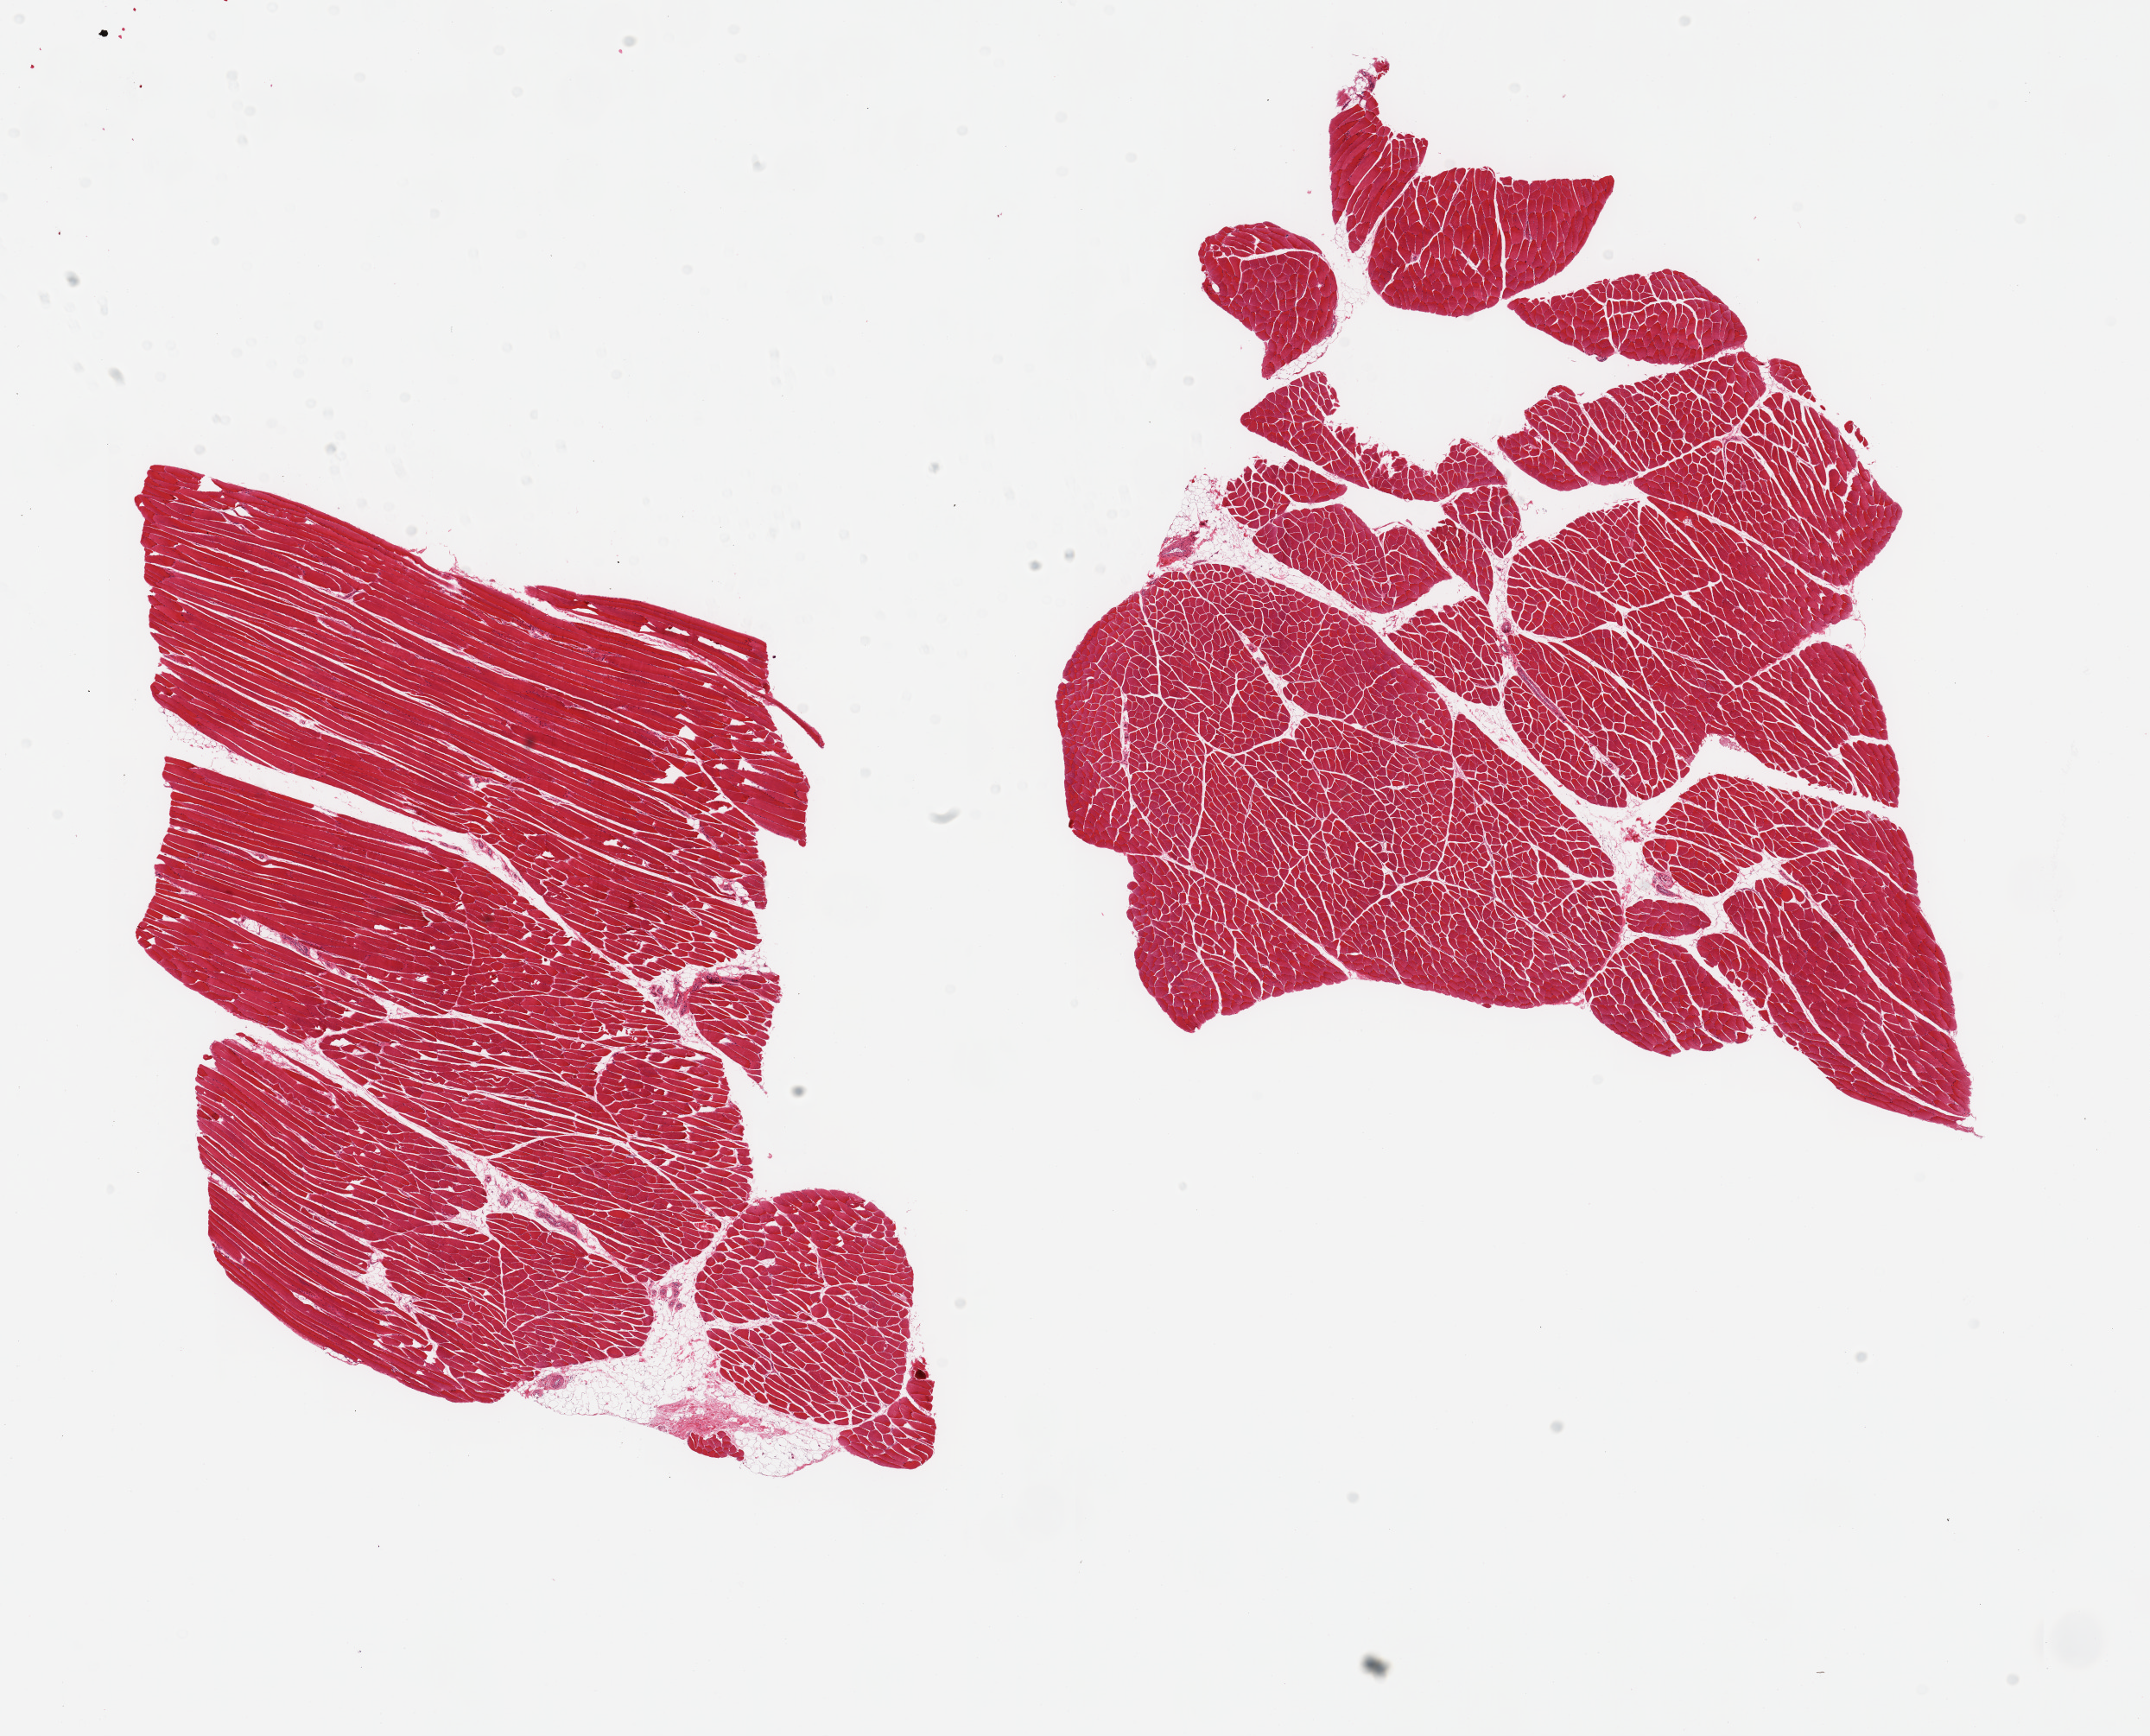
Whole-slide image, haematoxylin and eosin stain, low-resolution overview of the scanned area, about 19.7 x 15.9 mm (acquisition: 20x scan). PAXgene-fixed paraffin-embedded (PFPE) section. Target tissue: skeletal muscle. Donor tissue sample.
- reviewer comment on this tissue sample: 2 pieces, trace interstitial fat